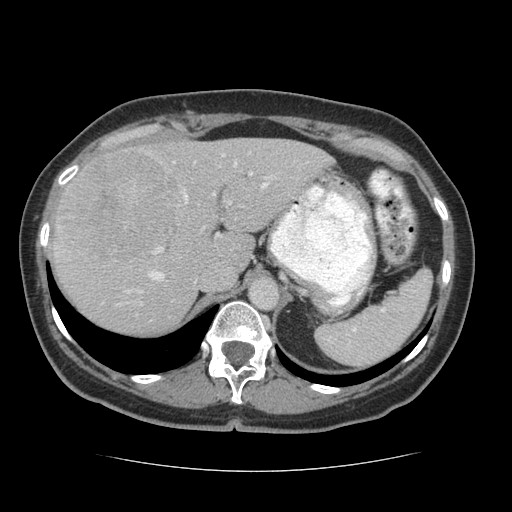
Contrast-enhanced abdominal CT (liver protocol), one axial slice. Slice 46 of 75 in the series (ordered by position). Reconstruction kernel STANDARD. 140 kVp. Soft-tissue window (W 400 / L 40 HU). 2.5 mm slice thickness. 512 × 512 image matrix, field of view 360 × 360 mm. Case-level facts recorded for this patient, not image findings: diagnosis: hepatocellular carcinoma (patient treated with transarterial chemoembolisation; whether this scan precedes or follows treatment is not stated here); TNM stage (as recorded): Stage-I; Child-Pugh class: A.
Structures marked on this image (semi-automatic segmentation, software-assisted and operator-edited):
- liver parenchyma outside the tumour (the mass and vessels are separate outlines, so this box may not span the whole liver): bounding box [x1, y1, x2, y2] px = [52, 138, 332, 334]
- mass: [54, 147, 187, 261]
- liver vessels: [55, 153, 308, 306]